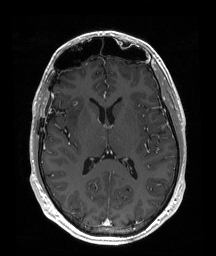
Brain MRI from a brain-tumour surgery series, one axial slice. T1-weighted post-contrast. 216 × 256 image matrix, field of view 219 × 260 mm. From the clinical record (not read from this slice): histopathology: Astrocytoma; WHO grade: 2; IDH mutation: yes; tumour location: Right Insular.
Annotated regions visible in this slice (expert manual segmentation):
- tumour: bounding box <67,98,84,127> (left, top, right, bottom; pixels)